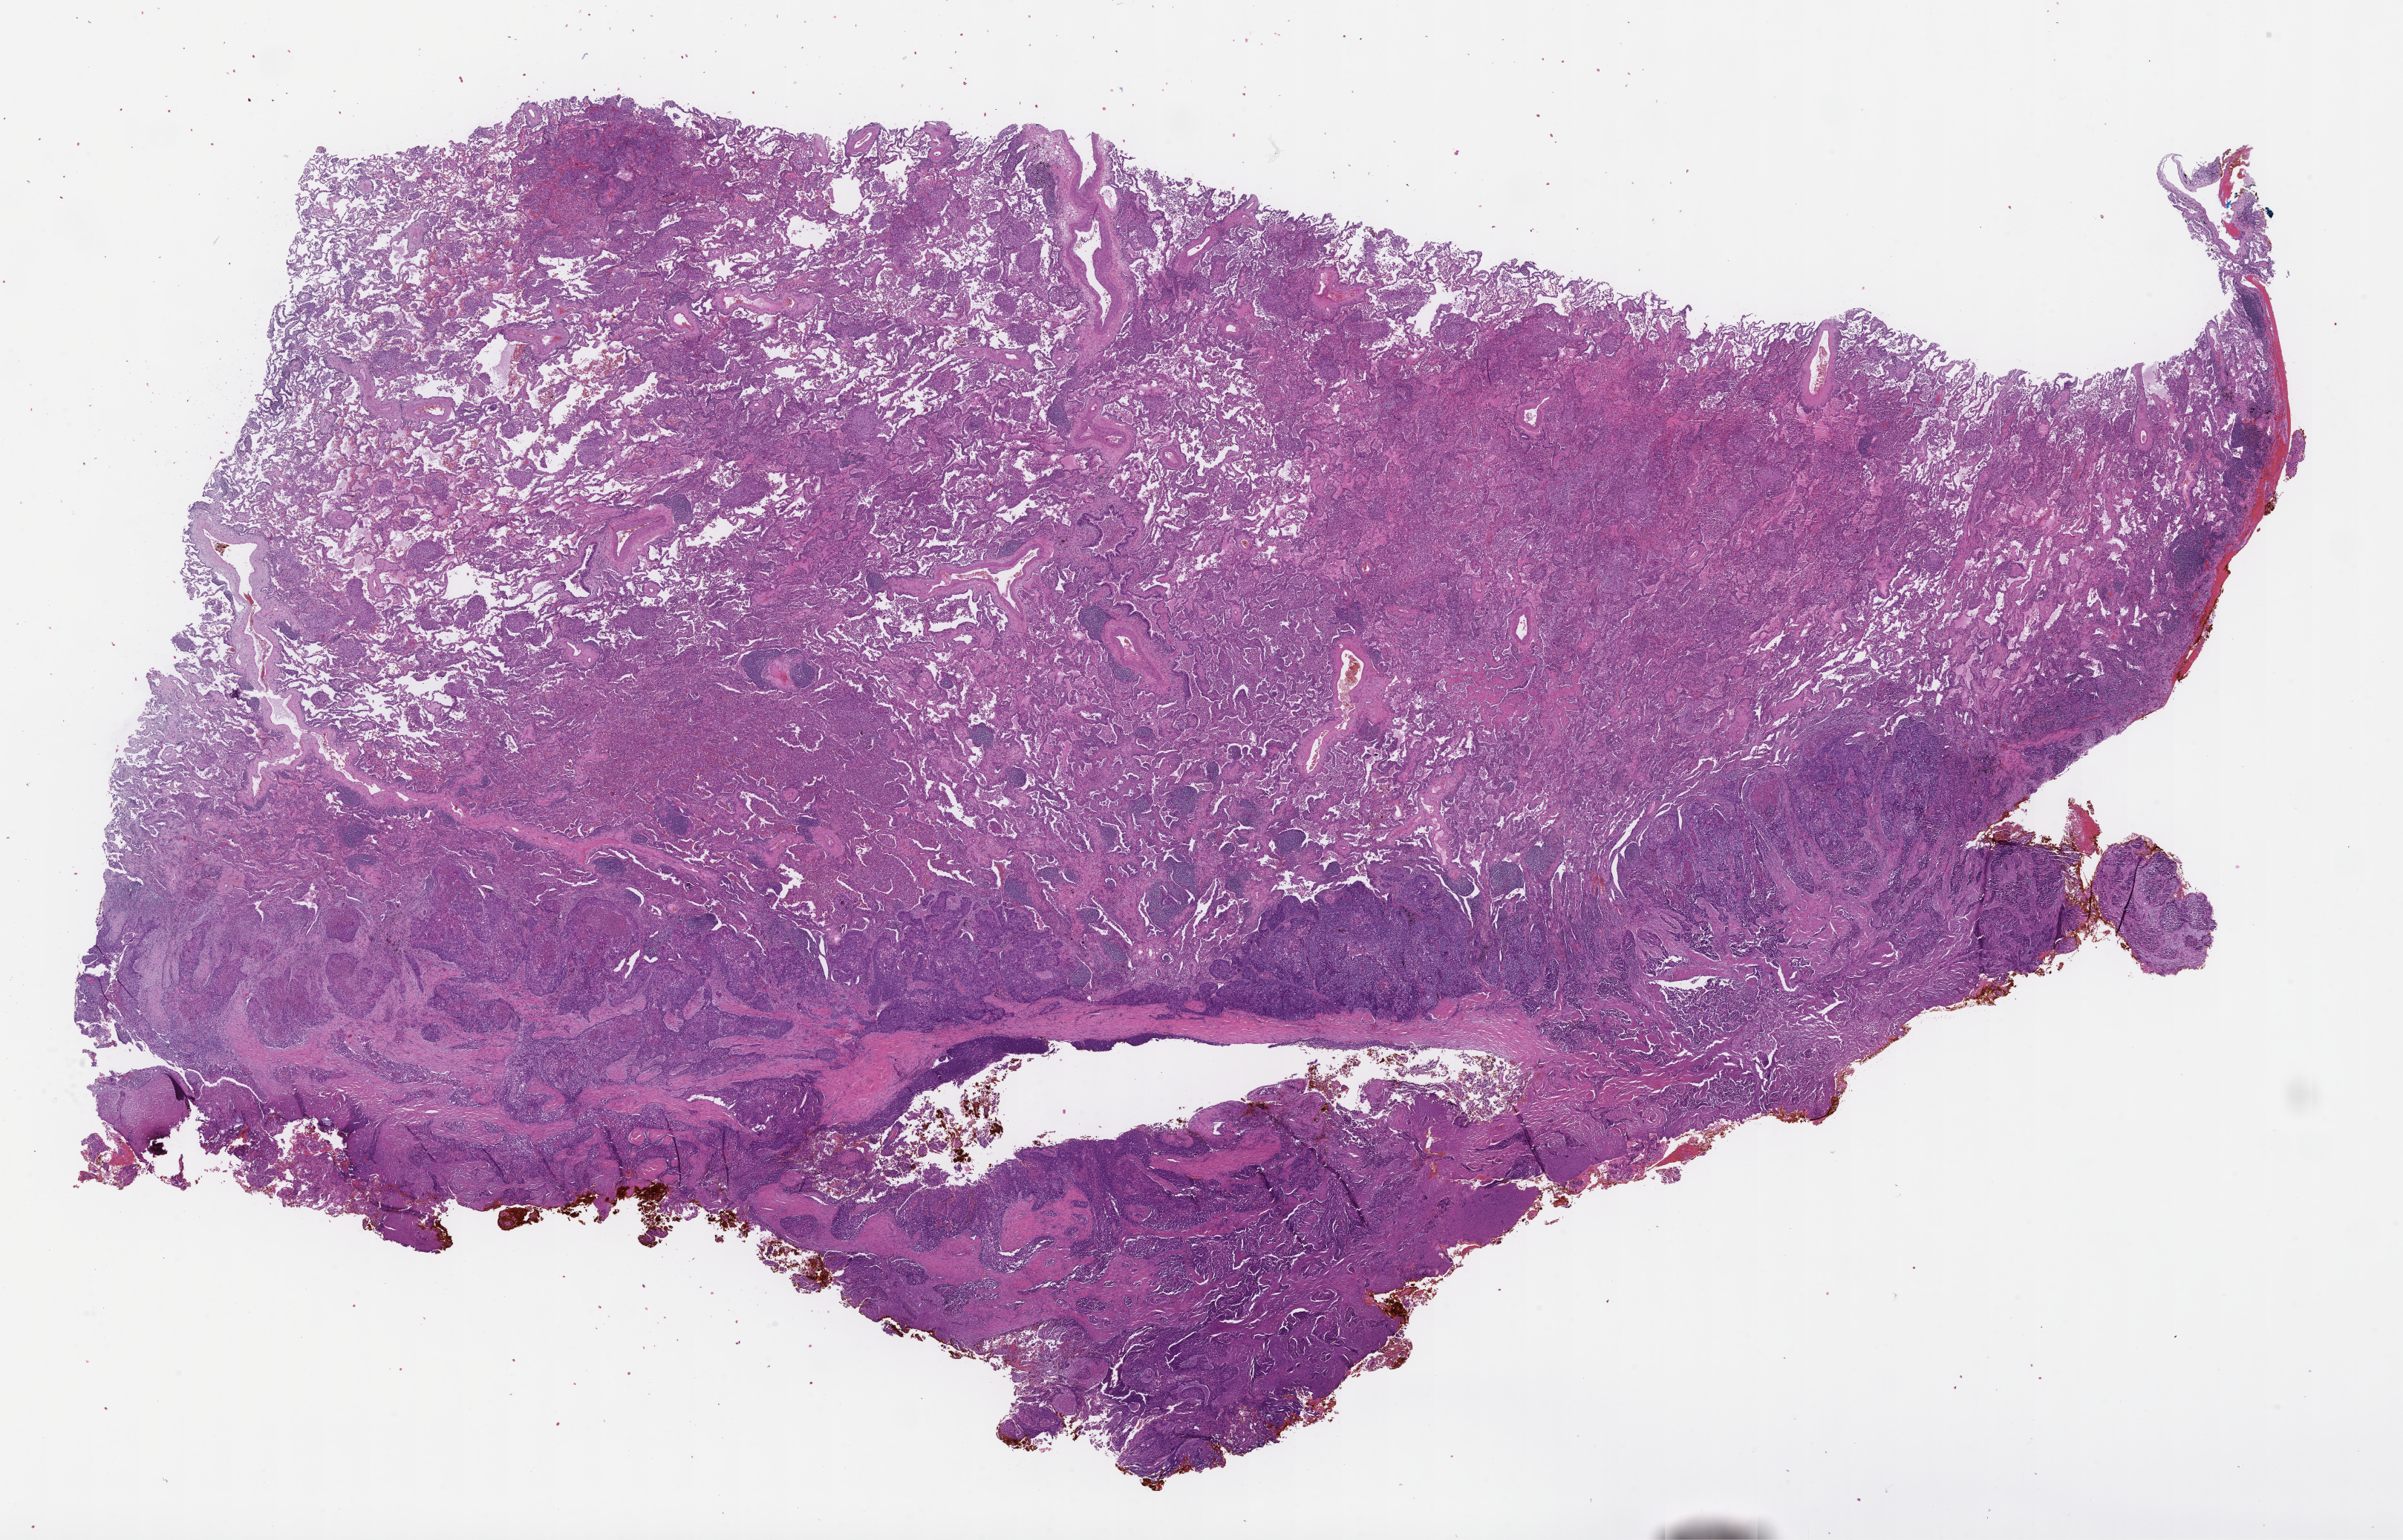
Whole-slide image, H&E stain, low-resolution overview of the scanned area, about 26.1 x 16.7 mm; formalin-fixed paraffin-embedded section; site: lung. Patient: female.
This section: primary tumor. Diagnosis: Non-Small Cell Lung Carcinoma.